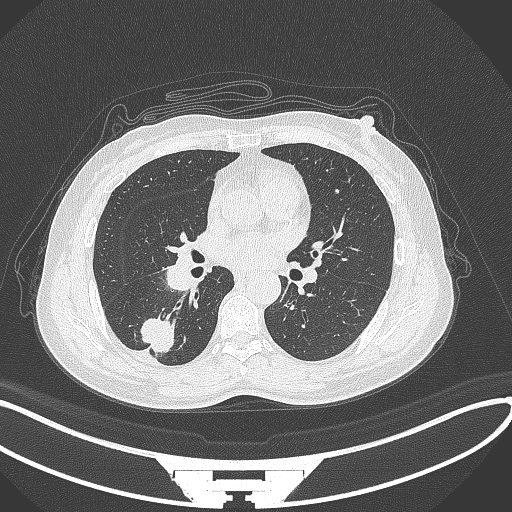
Chest CT, one axial slice; slice 153 of 352 in the series (ordered by position); lung window (W 1500 / L -600 HU); 1 mm slice thickness; 512 × 512 image matrix, field of view 400 × 400 mm. Patient: female, 55 years. From the clinical record (not read from this slice): clinical TNM (as recorded): T1c N1 M0.
Annotated regions visible in this slice (rectangle marked by the reading radiologist):
- lung tumour (recorded histology: adenocarcinoma): box from (x=140, y=317) to (x=176, y=359) px